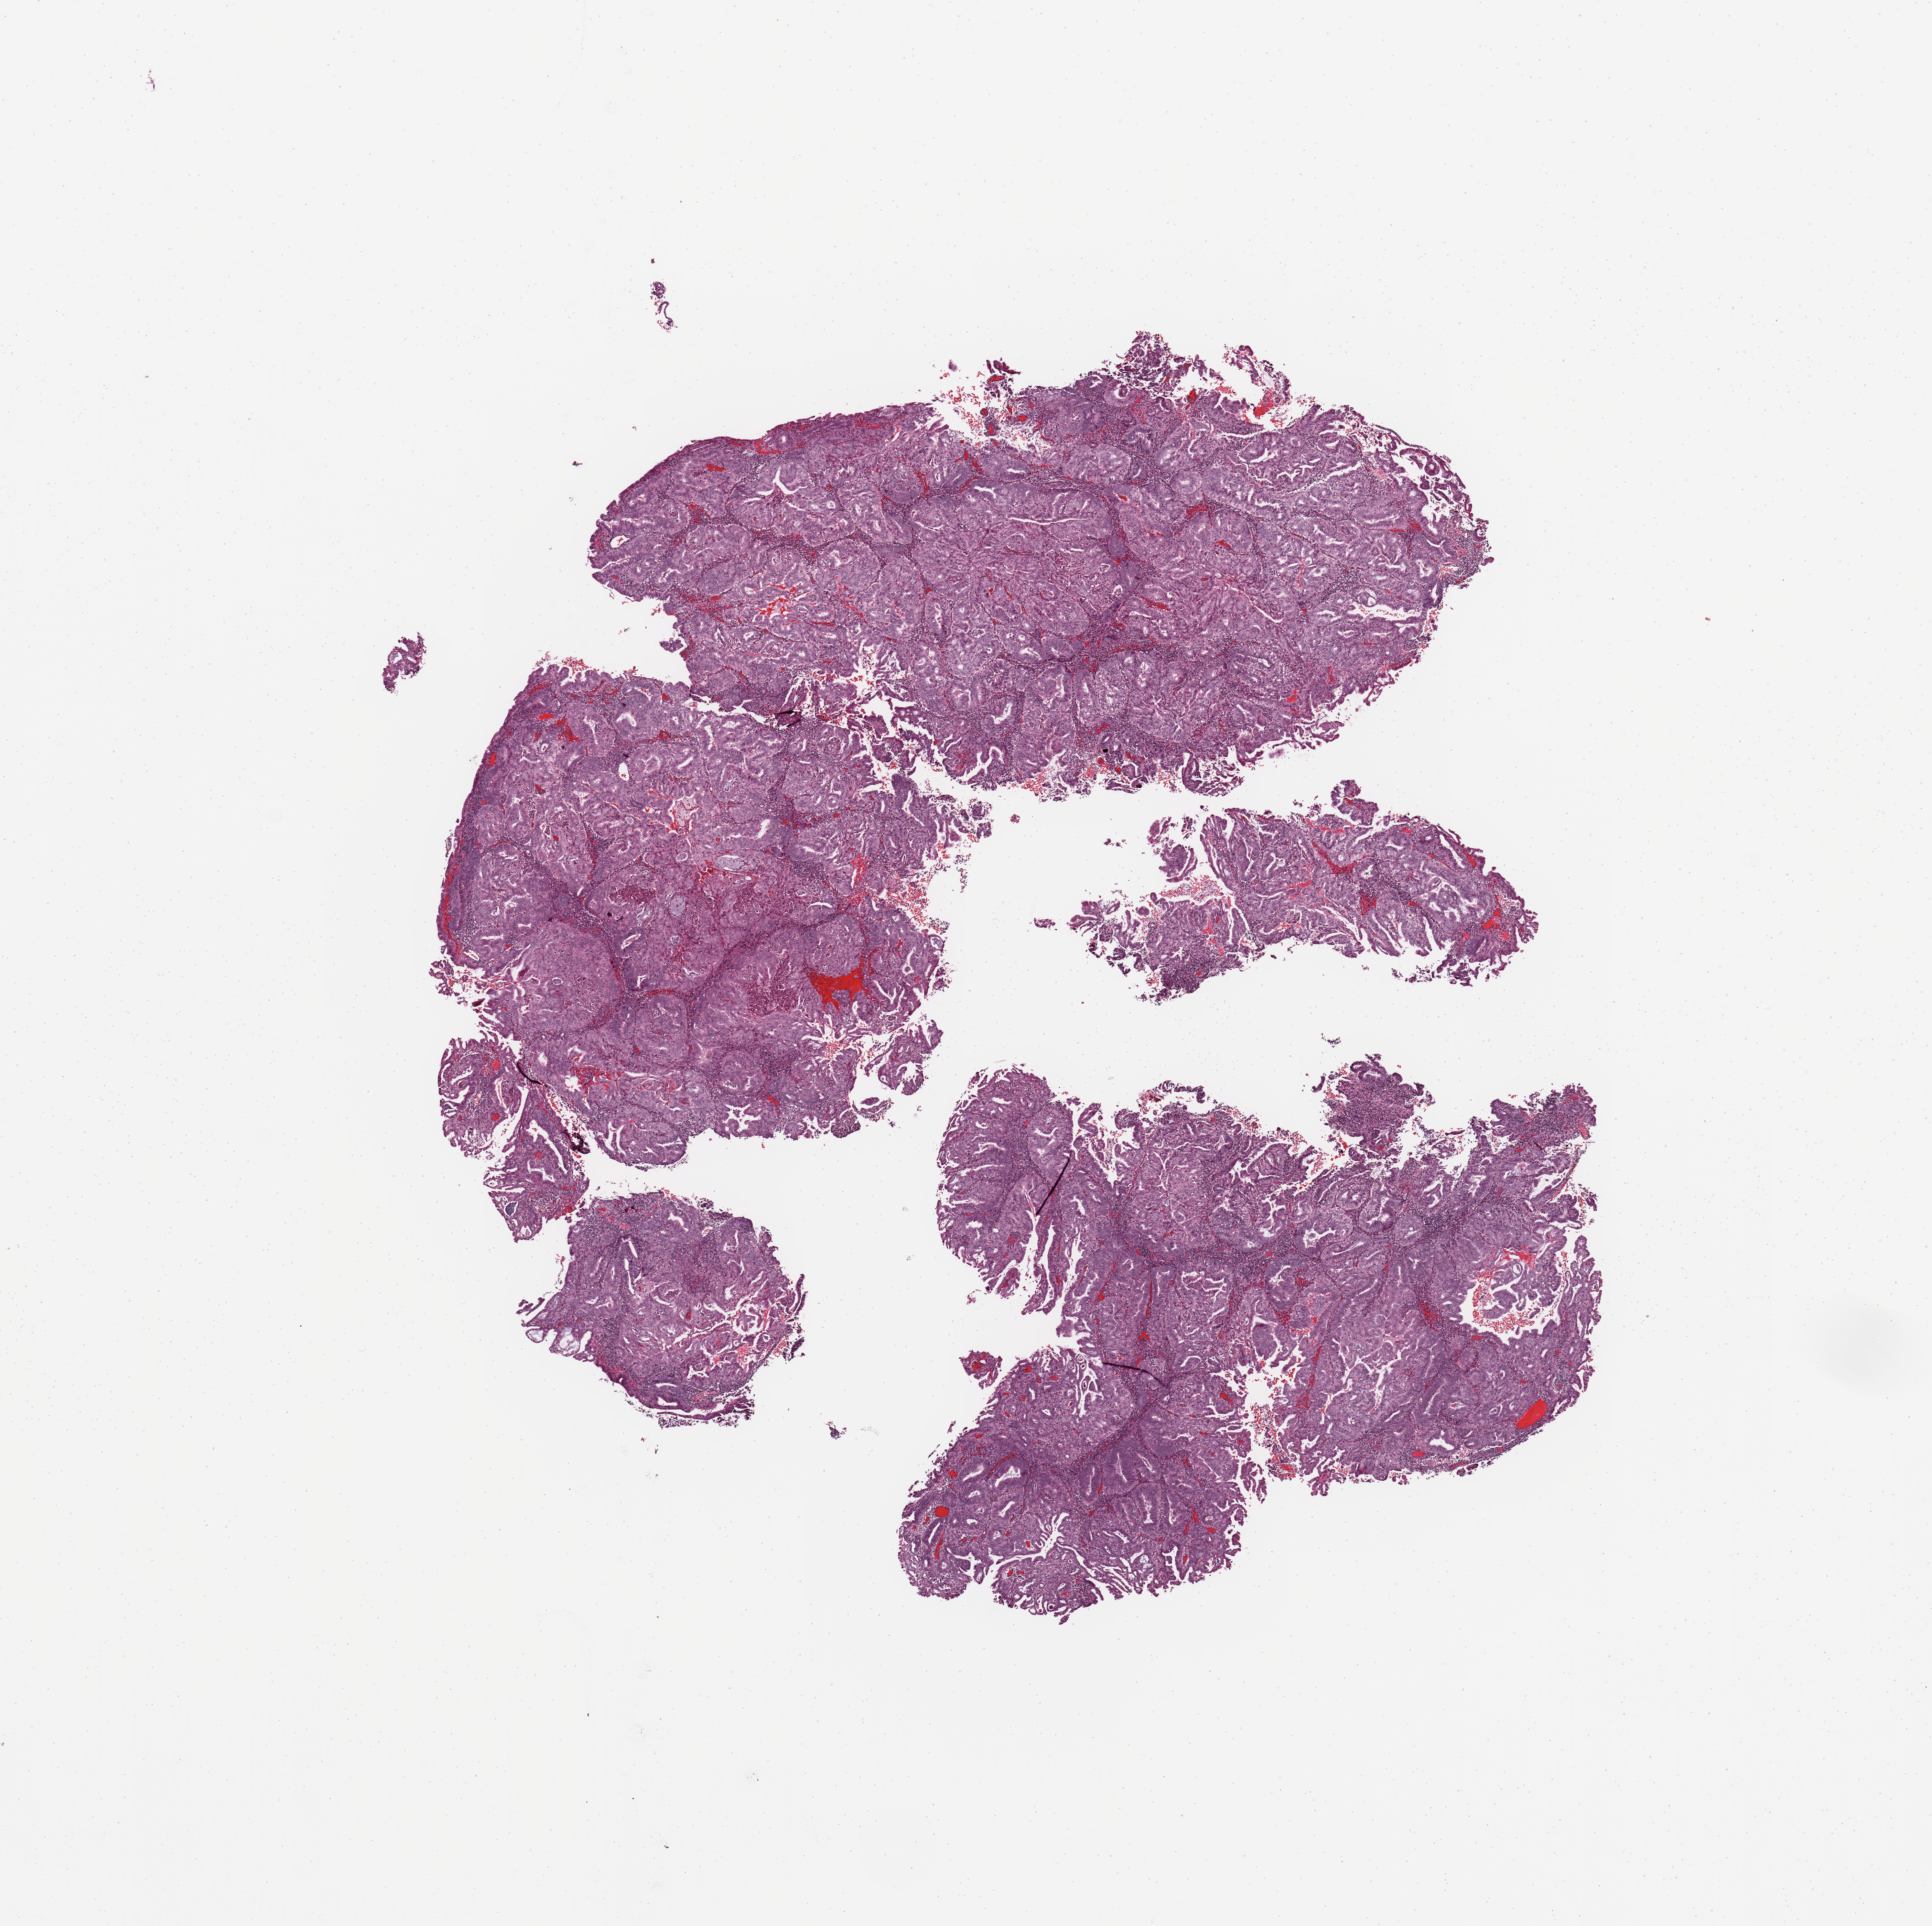
Whole-slide histology image, H&E, a low-resolution overview of the entire scanned area, about 11.8 x 11.8 mm (slide scanned at 20x). Tumour tissue sample, sampled site: uterus. 56-year-old female patient. Composition of this section per pathologist review: tumour nuclei 90%, necrosis 0%.
AJCC pathologic stage: I. Diagnosis: Endometrioid adenocarcinoma, NOS.